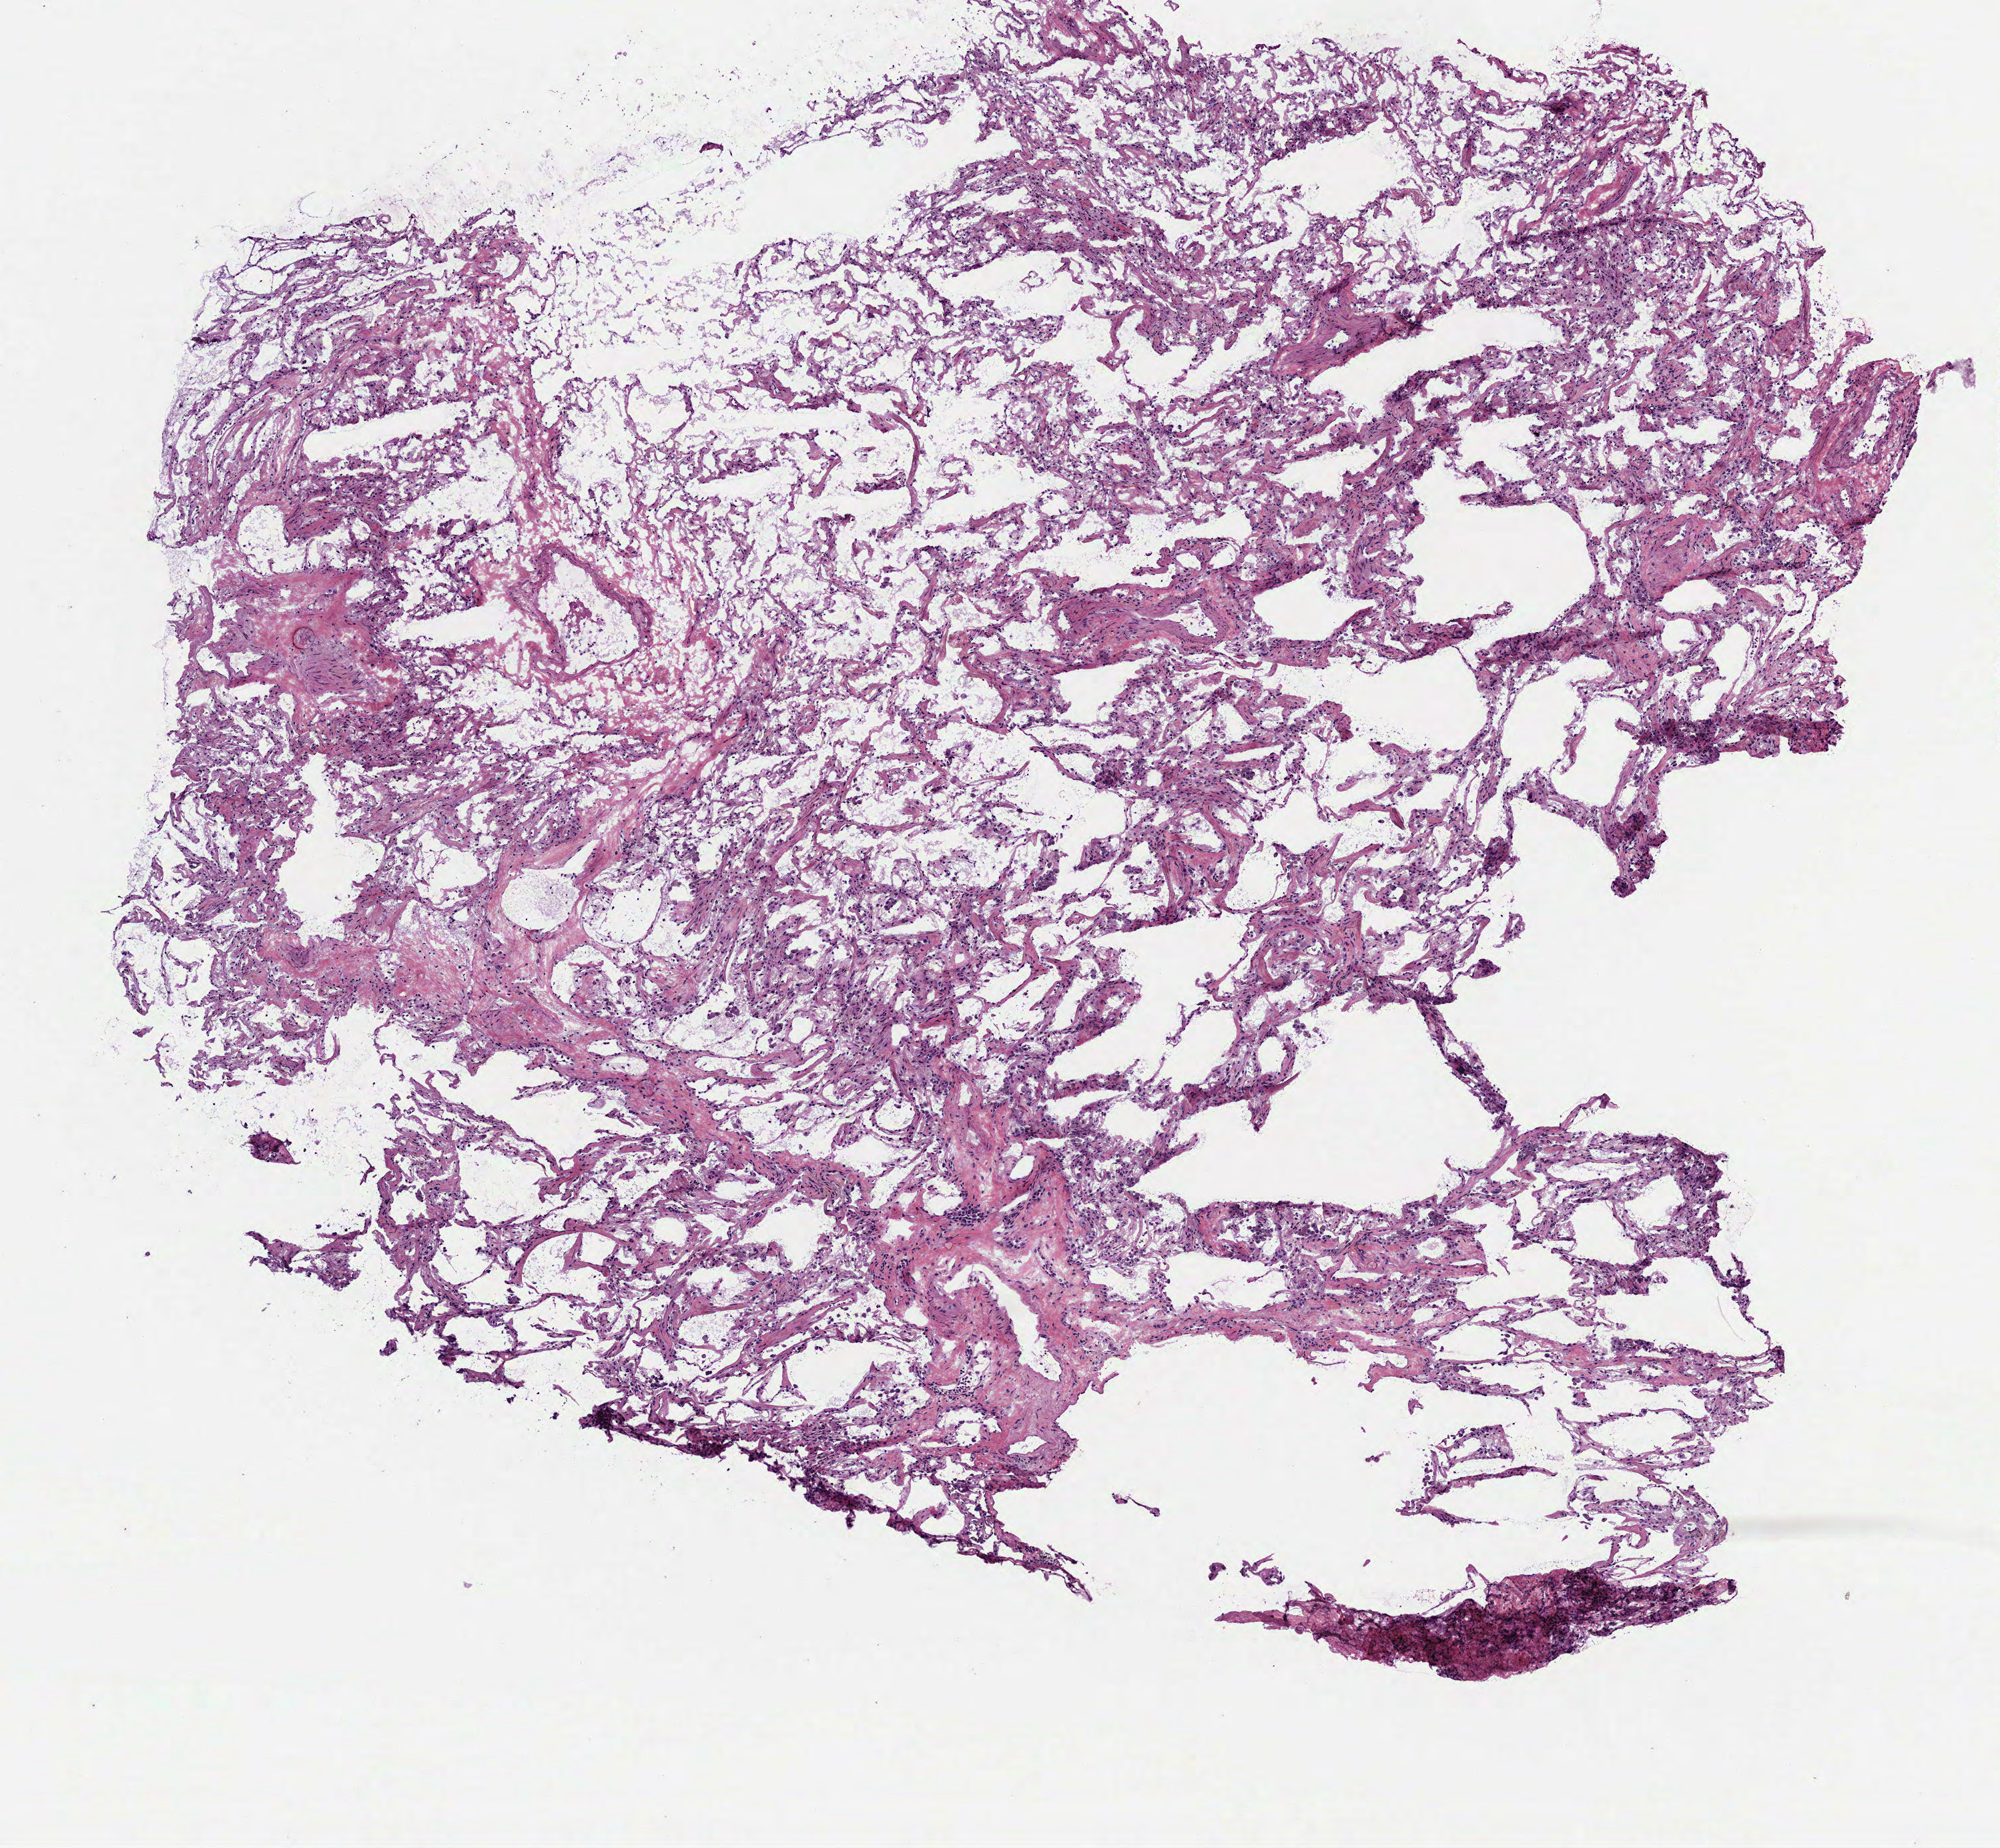
Hematoxylin and eosin (H&E) stained whole-slide image — whole scanned area (about 6.0 x 5.6 mm, acquisition: 40x scan) shown as a low-resolution overview, frozen section from the top of the tissue portion, solid tissue normal (non-tumour tissue) sample from the lung. Female patient; age at initial diagnosis 64 years.
- this section: solid tissue normal (non-tumour) sample from the same patient
- patient diagnosis: Adenocarcinoma, NOS (upper lobe, lung)